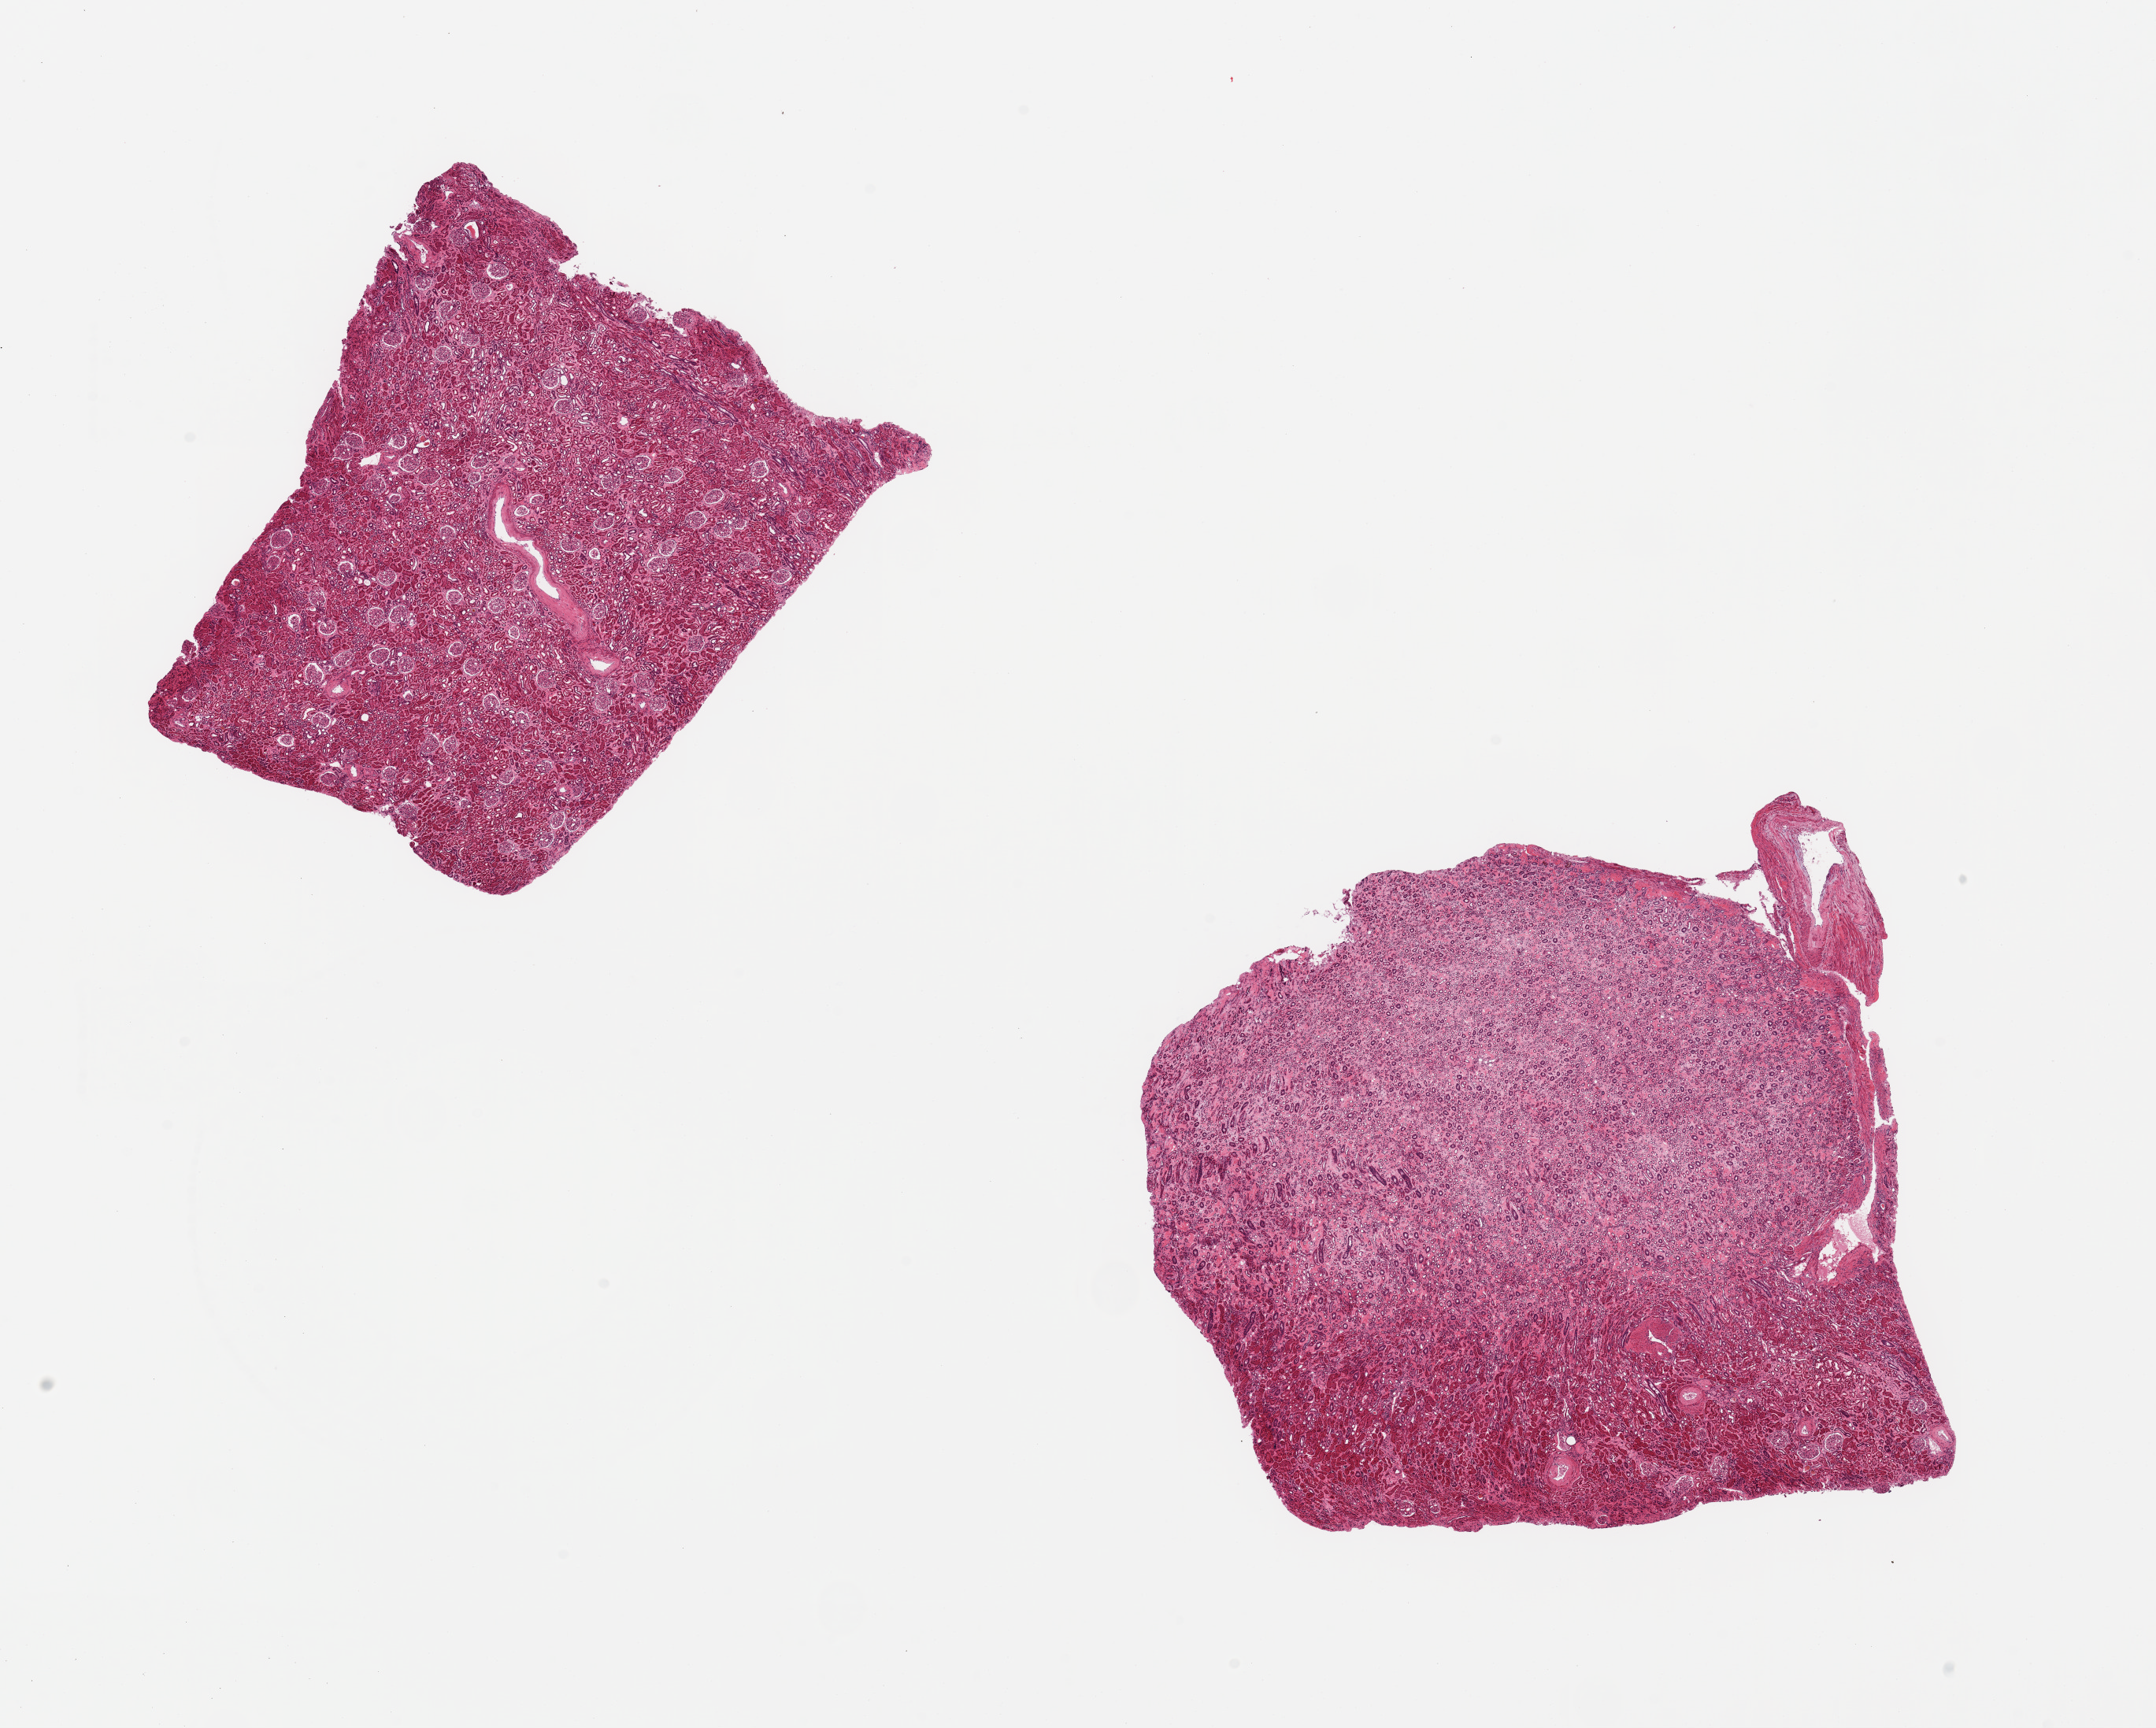
H&E whole-slide image, whole scanned area (about 21.7 x 17.4 mm, slide scanned at 20x) shown as a low-resolution overview, PAXgene-fixed, paraffin-embedded tissue, sampled site (target tissue): renal medulla, tissue donor sample.
Review note (as recorded): 2 ~6.5x5mm pieces. One contains glomeruli (cortex), the other nearly pure tubules with a few glomeruli.